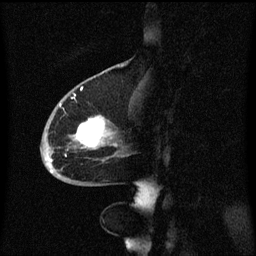
Breast MRI (dynamic contrast-enhanced), one sagittal slice. Slice 23 of 60 in the series (ordered by position). Dynamic contrast-enhanced series, image 2 of 3 at this slice position (ordered by acquisition). 1.5 T. TE 4.2 ms, TR 8.4 ms. 2 mm slice thickness. 256 × 256 image matrix. Patient: female, 68 years. From the clinical record (not read from this slice): setting: breast cancer imaged before/during neoadjuvant chemotherapy; receptor status: triple-negative.
Structures marked on this image (semi-automatic segmentation, software-assisted and operator-edited):
- analysis volume of interest (the breast-tissue region the enhancement analysis was run in; not a lesion): box from (x=41, y=94) to (x=129, y=173) px
- tumour enhancement mask (voxels above the 70 % enhancement threshold inside the analysis volume of interest): (x=46, y=104)–(x=113, y=173)